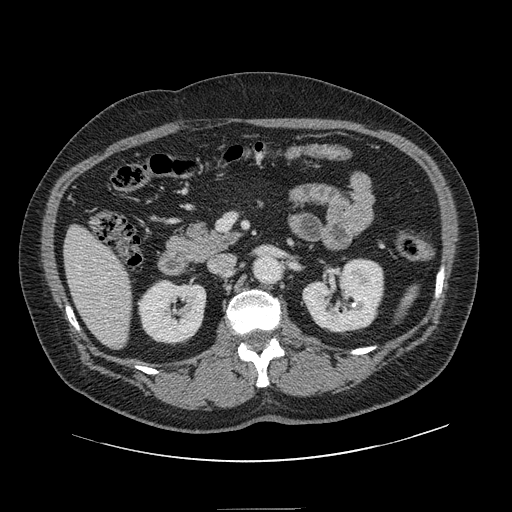
Contrast-enhanced abdominal CT, one axial slice. Position 55 of 154 along the scan axis. Intravenous contrast given. Soft-tissue window (W 400 / L 40 HU). 512 × 512 image matrix, field of view 451 × 451 mm. Male patient, age 61 years. From the clinical record (not read from this slice): diagnosis: colorectal cancer liver metastases, imaged before liver resection; multiple liver metastases: yes; largest metastasis: 2.6 cm.
Outlined on this slice (manually delineated by an expert):
- hepatic veins: bounding box [x1, y1, x2, y2] px = [77, 266, 104, 301]
- liver: [65, 227, 132, 348]
- planned liver remnant (the part of the liver to remain after resection): [65, 227, 132, 349]